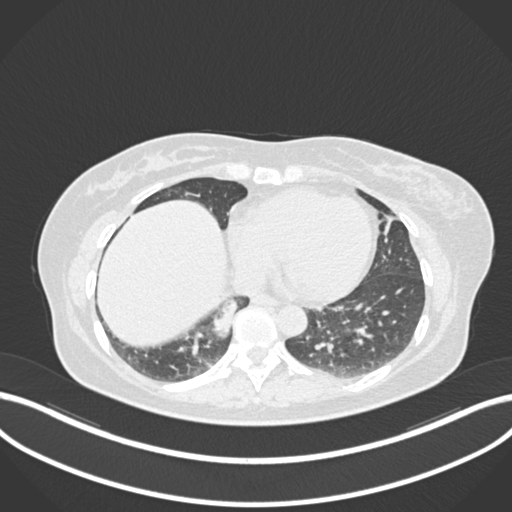
Chest CT, one axial slice. Reconstruction kernel B30f. 120 kVp. Lung window (W 1500 / L -600 HU). 1 mm slice thickness. 512 × 512 image matrix, field of view 400 × 400 mm. Female patient, age 54 years. From the clinical record (not read from this slice): clinical TNM (as recorded): T4 N0 M0.
Structures marked on this image (rectangle marked by the reading radiologist):
- lung tumour (recorded histology: adenocarcinoma): box from (x=205, y=290) to (x=241, y=342) px